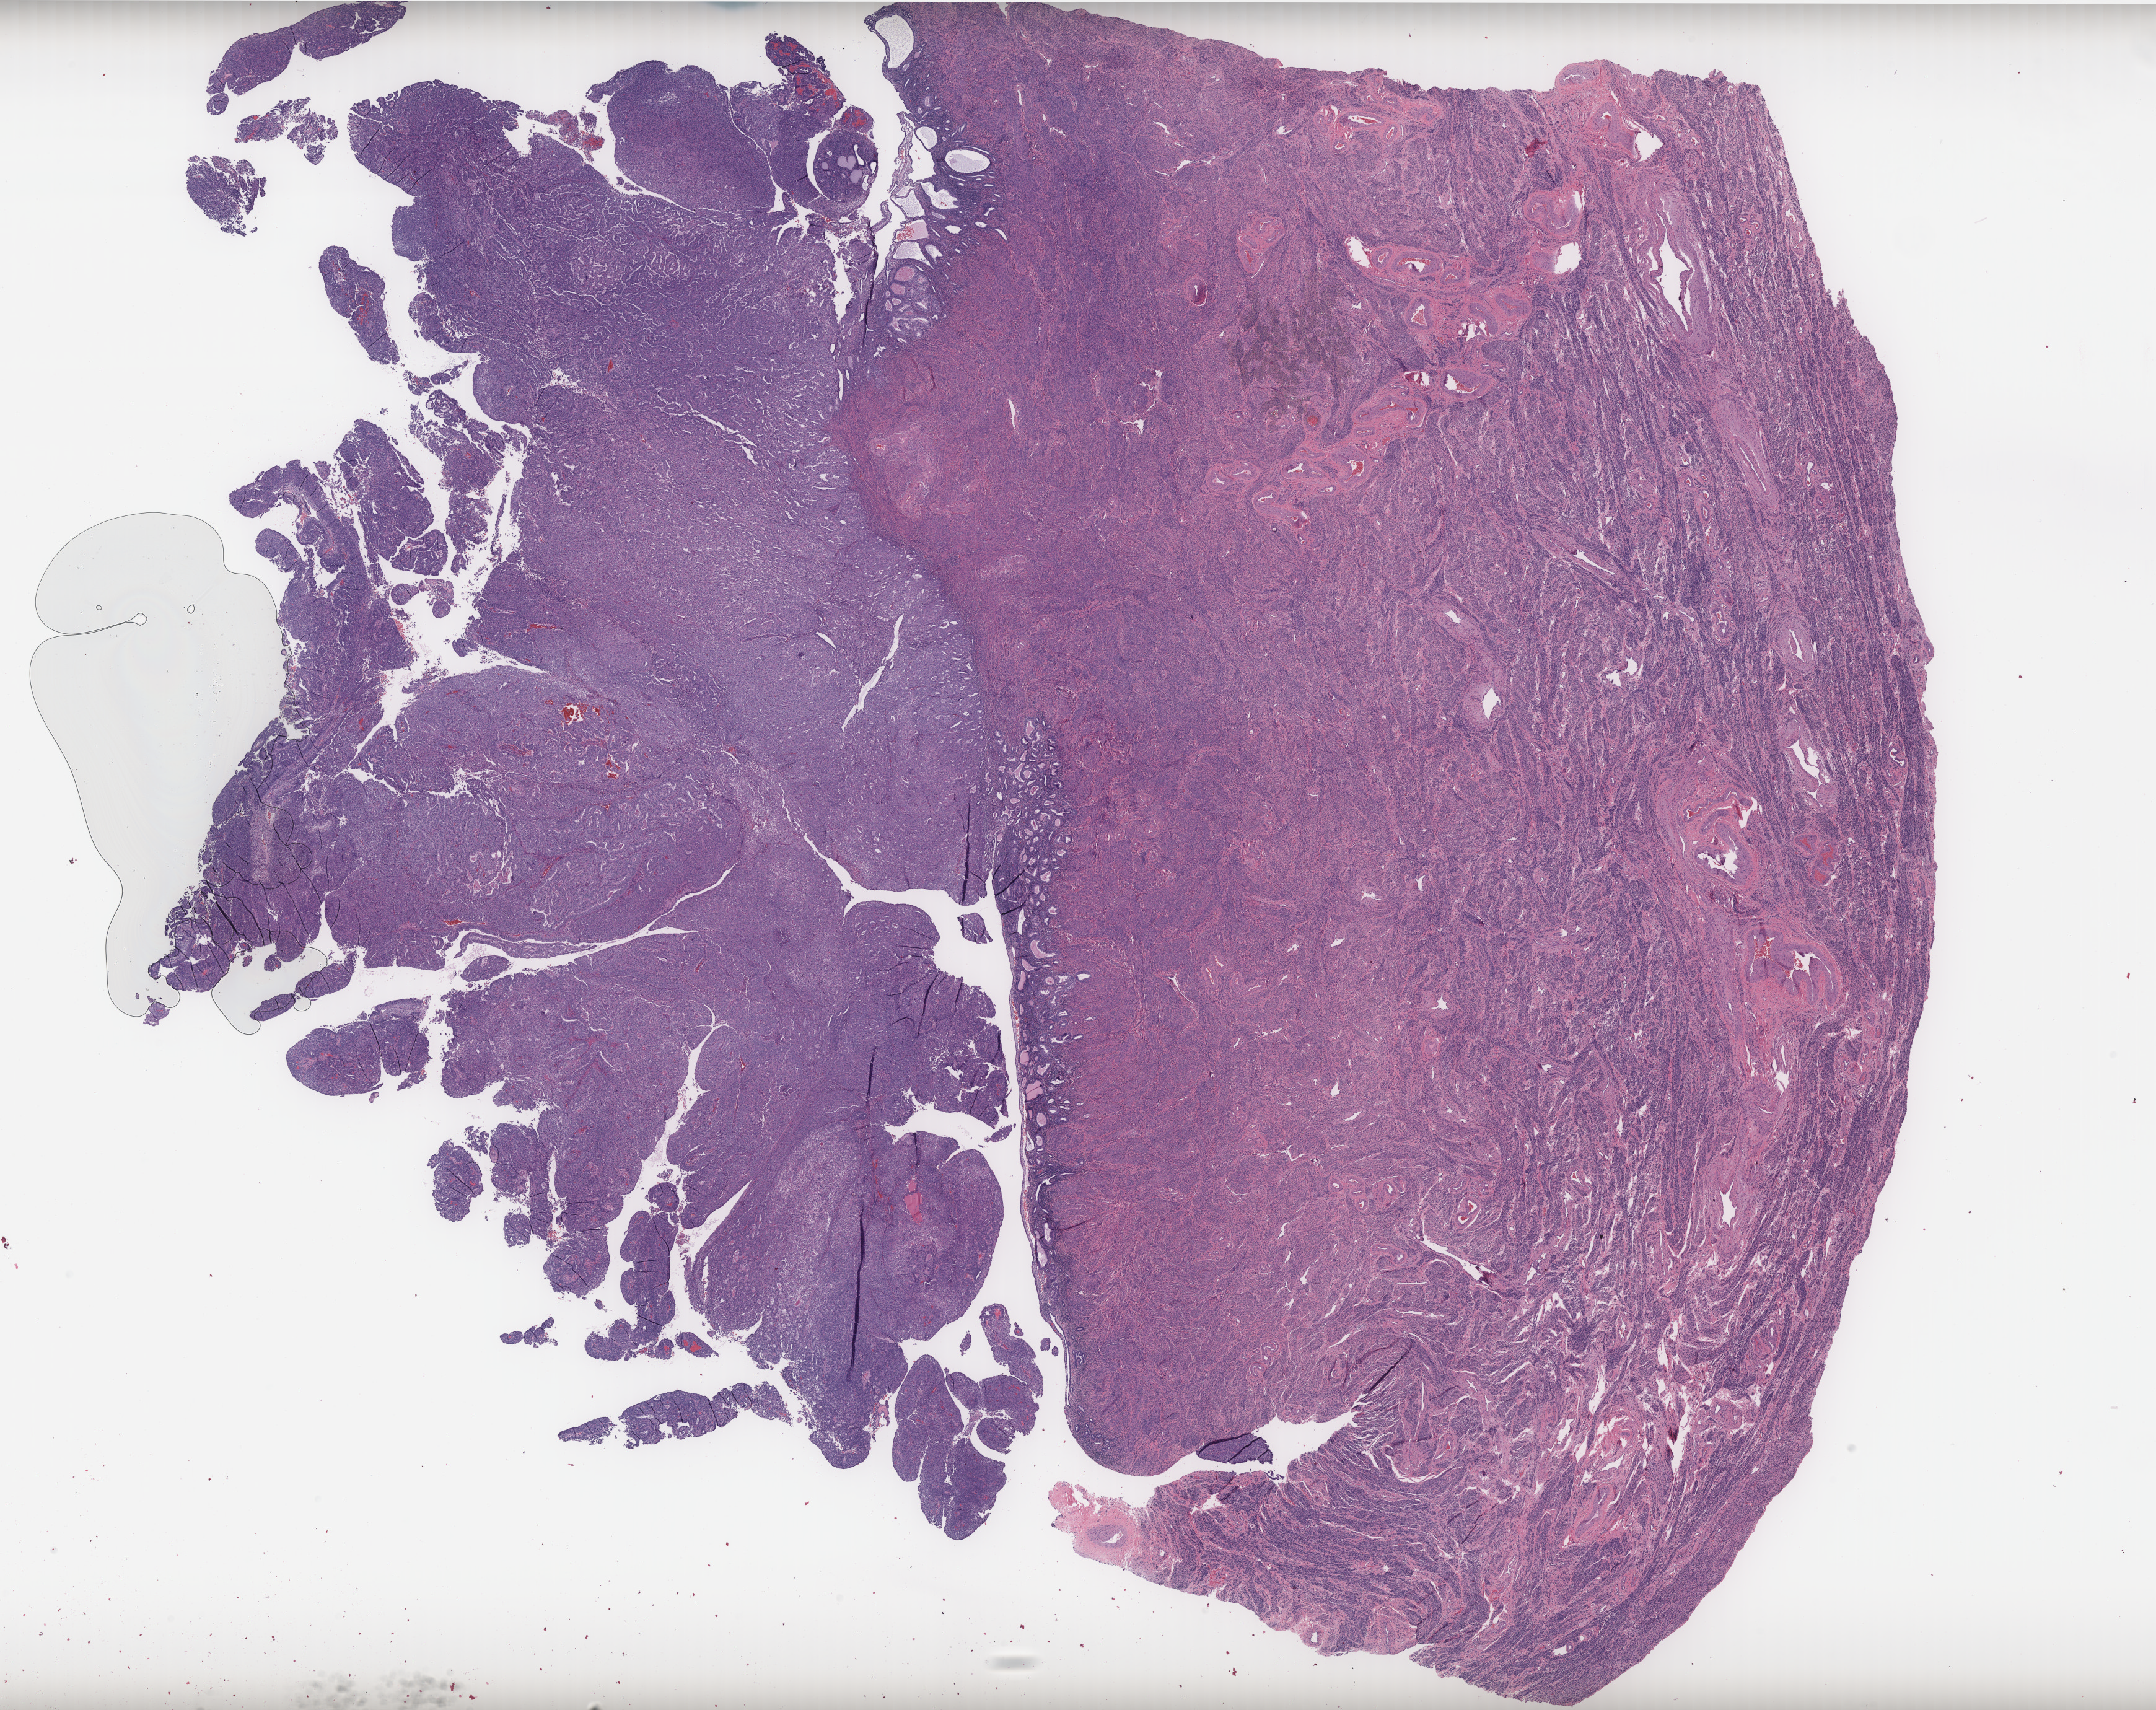
Digitized H&E tissue section (whole slide) — a low-resolution overview of the entire scanned area, about 27.9 x 22.1 mm. Formalin-fixed paraffin-embedded (FFPE) diagnostic section. Uterus, primary tumour sample. Patient: female, age at initial diagnosis 60 years.
Histologic diagnosis: Endometrioid adenocarcinoma, NOS.